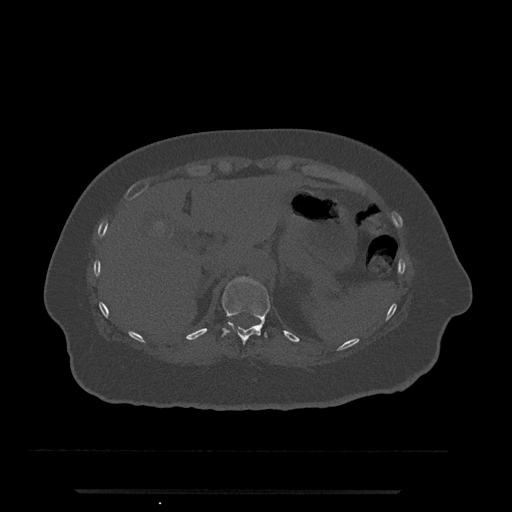
CT including the spine, one axial slice. Position 225 of 797 along the scan axis. Reconstruction kernel Br40s/3. Bone window (W 1800 / L 400 HU). 0.5 mm slice thickness. 512 × 512 image matrix. Female patient, age 51 years. From the clinical record (not read from this slice): primary cancer: neuro.
Annotated regions visible in this slice (semi-automatically segmented with operator editing):
- T11 vertebra: bounding box [x1, y1, x2, y2] px = [222, 277, 270, 345]